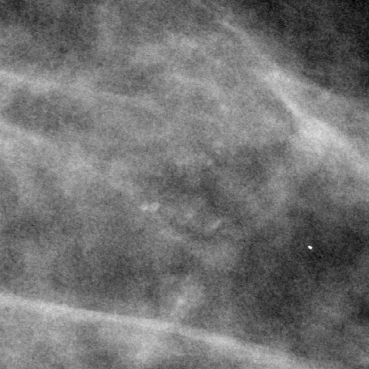
Region of interest cut from a scanned film mammogram (one marked finding); left breast; CC view.
Finding: calcifications, morphology round and regular / amorphous; BI-RADS assessment category 4; pathology result (as recorded, not read from the image): benign.